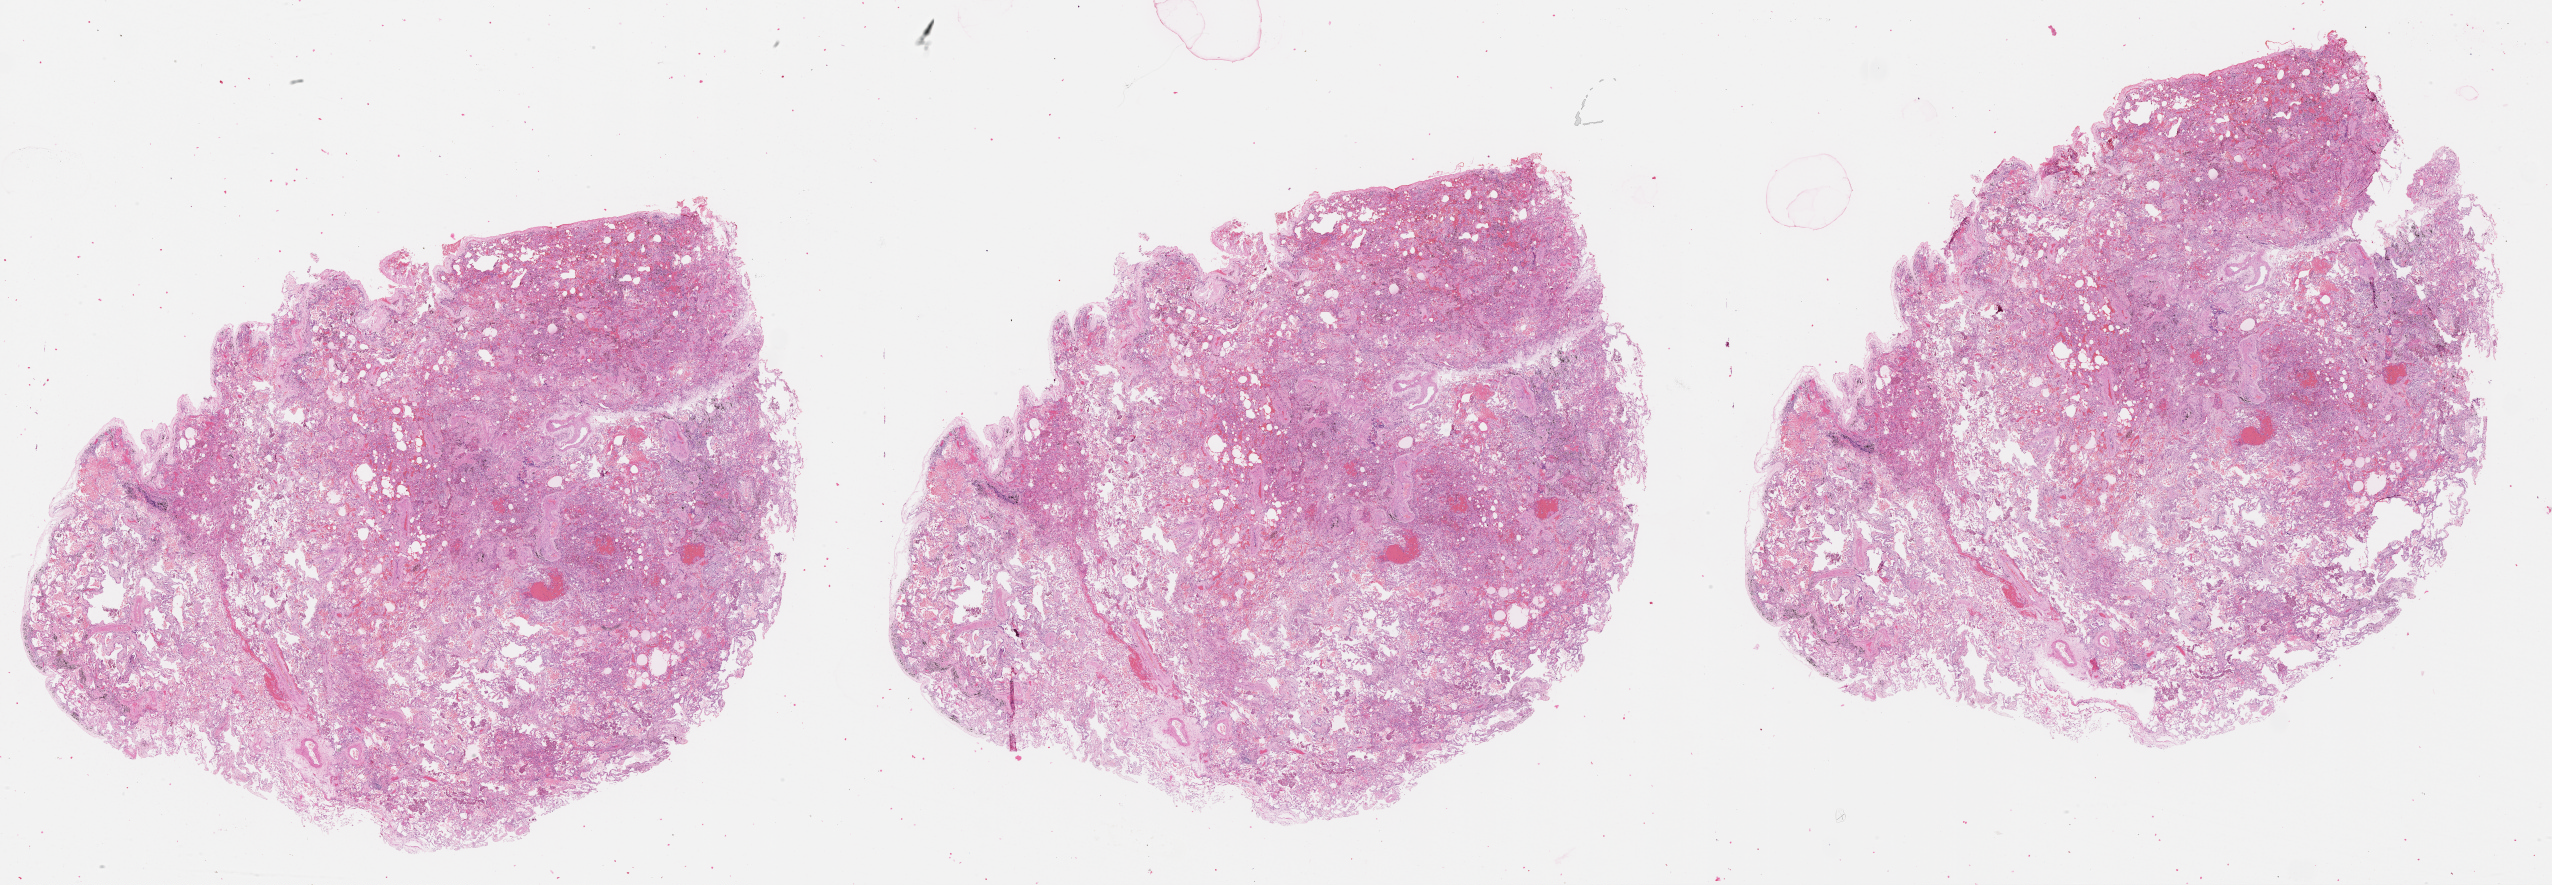
Digitized Hematoxylin and eosin (H&E) stained tissue section (whole slide), whole scanned area (about 41.1 x 14.2 mm, slide scanned at 20x) shown as a low-resolution overview. Normal (non-tumour) tissue sample, lung. 57-year-old male patient.
This section: normal (non-tumour) tissue from the same patient. Patient diagnosis (cohort enrolment): squamous cell carcinoma (lung).